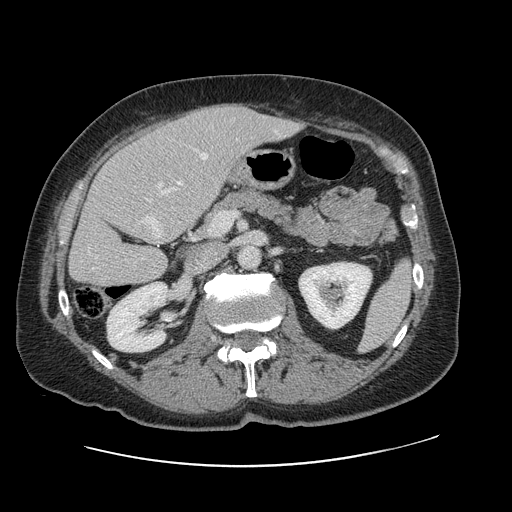
Contrast-enhanced abdominal CT, one axial slice; position 47 of 138 along the scan axis; 120 kVp; soft-tissue window (W 400 / L 40 HU); 2.5 mm slice thickness; 512 × 512 image matrix, field of view 402 × 402 mm. Male patient, age 71 years. From the clinical record (not read from this slice): diagnosis: colorectal cancer liver metastases, imaged before liver resection; multiple liver metastases: no.
Outlined on this slice (manually delineated by an expert):
- hepatic veins: bounding box (x1, y1, x2, y2) in pixels: (88, 153, 208, 269)
- liver: (70, 105, 298, 288)
- planned liver remnant (the part of the liver to remain after resection): (70, 139, 197, 288)
- portal vein (with intrahepatic branches): (148, 183, 162, 201)